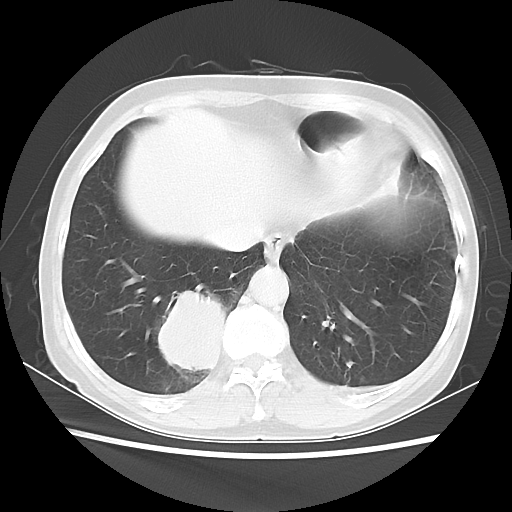
Chest CT, one axial slice; slice 13 of 56 in the series (ordered by position); 120 kVp; lung window (W 1500 / L -600 HU); 5 mm slice thickness; 512 × 512 image matrix. Female patient, age 66 years. From the clinical record (not read from this slice): clinical TNM (as recorded): T2 N3 M0; histopathological grade: G3.
Annotated regions visible in this slice (bounding box drawn by a radiologist):
- lung tumour (recorded histology: small cell carcinoma): bounding box [x1, y1, x2, y2] px = [146, 272, 237, 388]